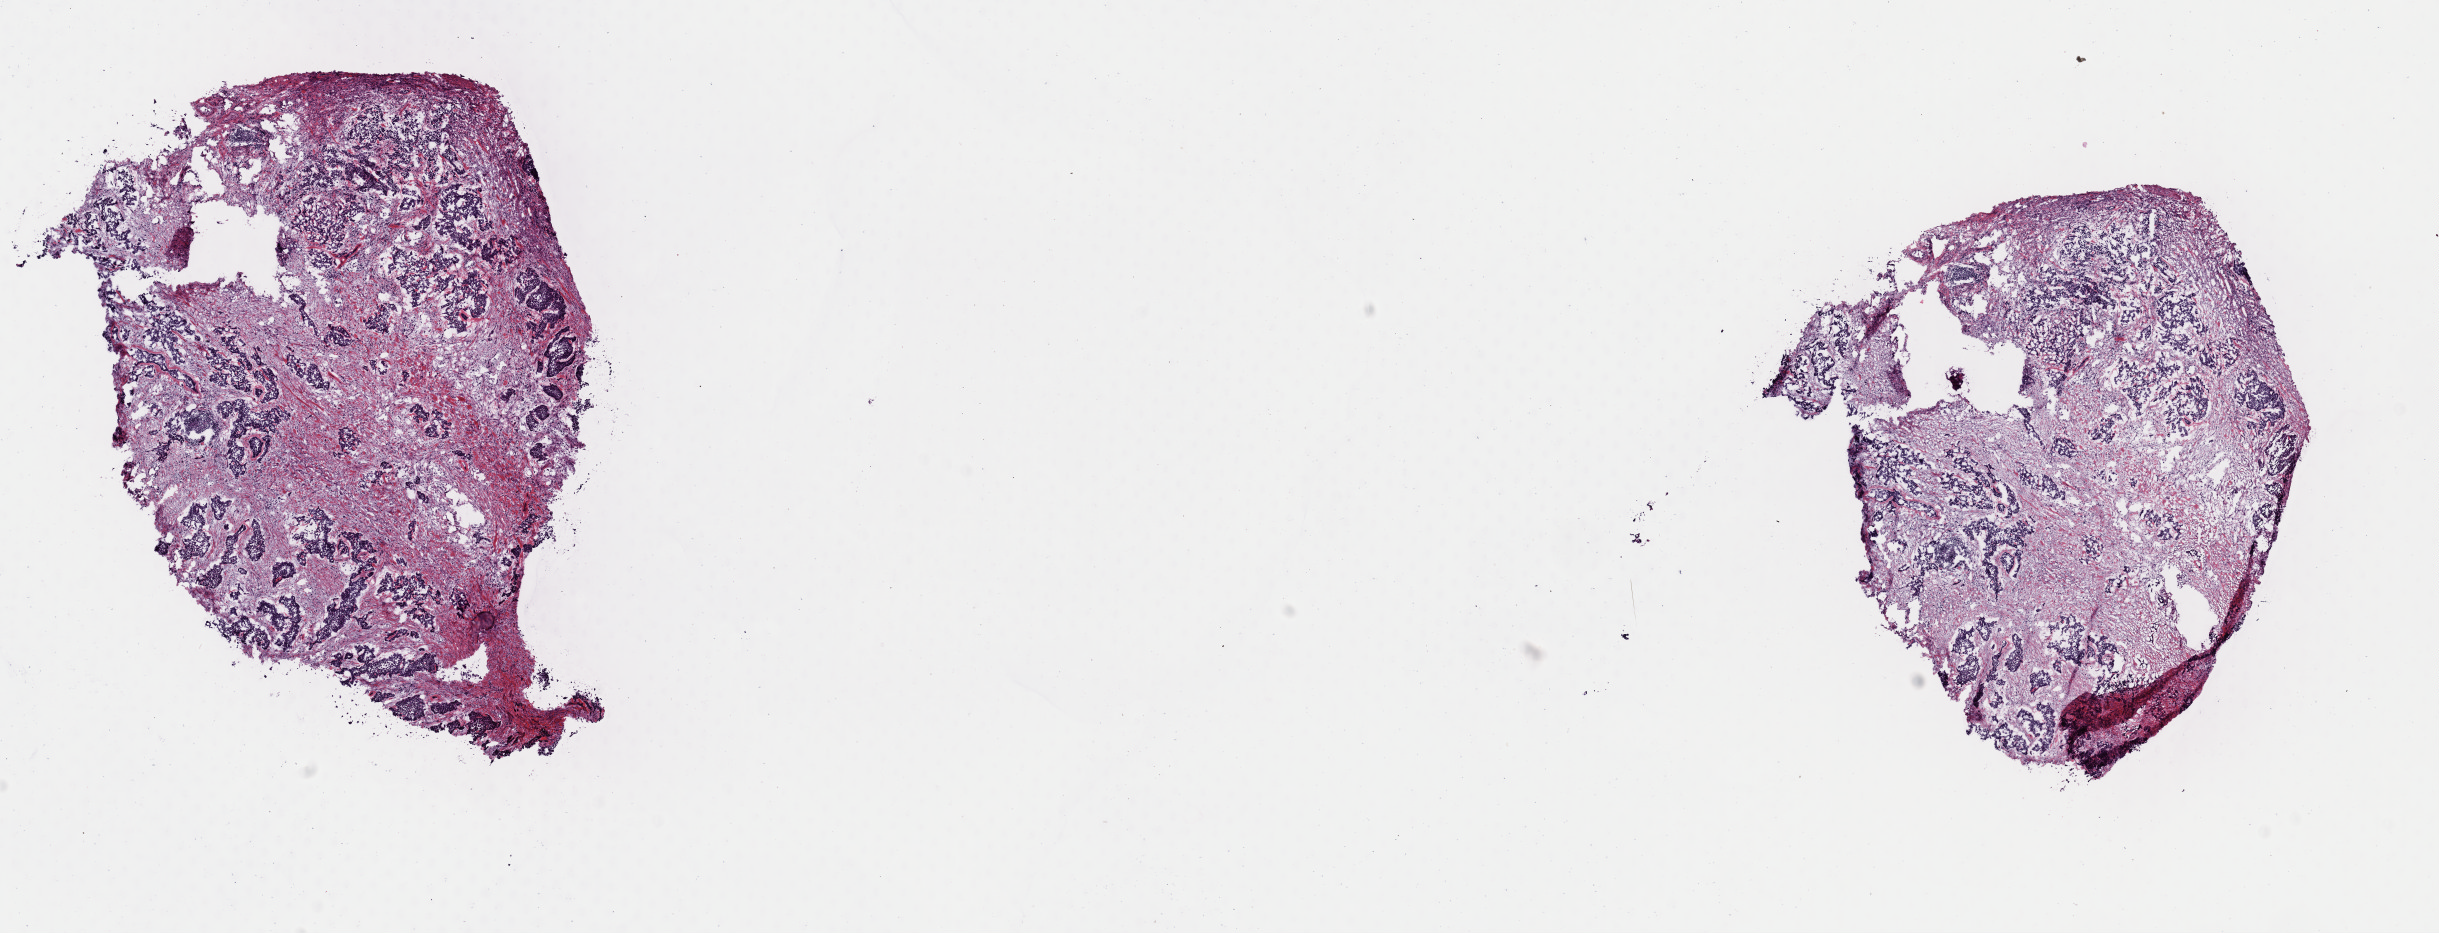
Digitized Hematoxylin and eosin (H&E) stained tissue section (whole slide) — shown as a low-resolution overview of the whole scanned area (about 19.3 x 7.4 mm). Frozen section from the top of the tissue portion. Bladder, primary tumour sample. Male, age 59 years at initial diagnosis. Histologic grade: high grade. Slide review estimates, as recorded: tumour cells 70%, tumour nuclei 60%, normal cells 30%, stromal cells 0%, necrosis 0%. Inflammatory infiltration, as recorded: lymphocyte infiltration 1%, monocyte infiltration 0%, neutrophil infiltration 0%.
- lymph nodes positive (case pathology): 1 of 14 examined
- AJCC pathologic stage: IV (7th edition)
- pathologic diagnosis: Papillary transitional cell carcinoma (lateral wall of bladder)